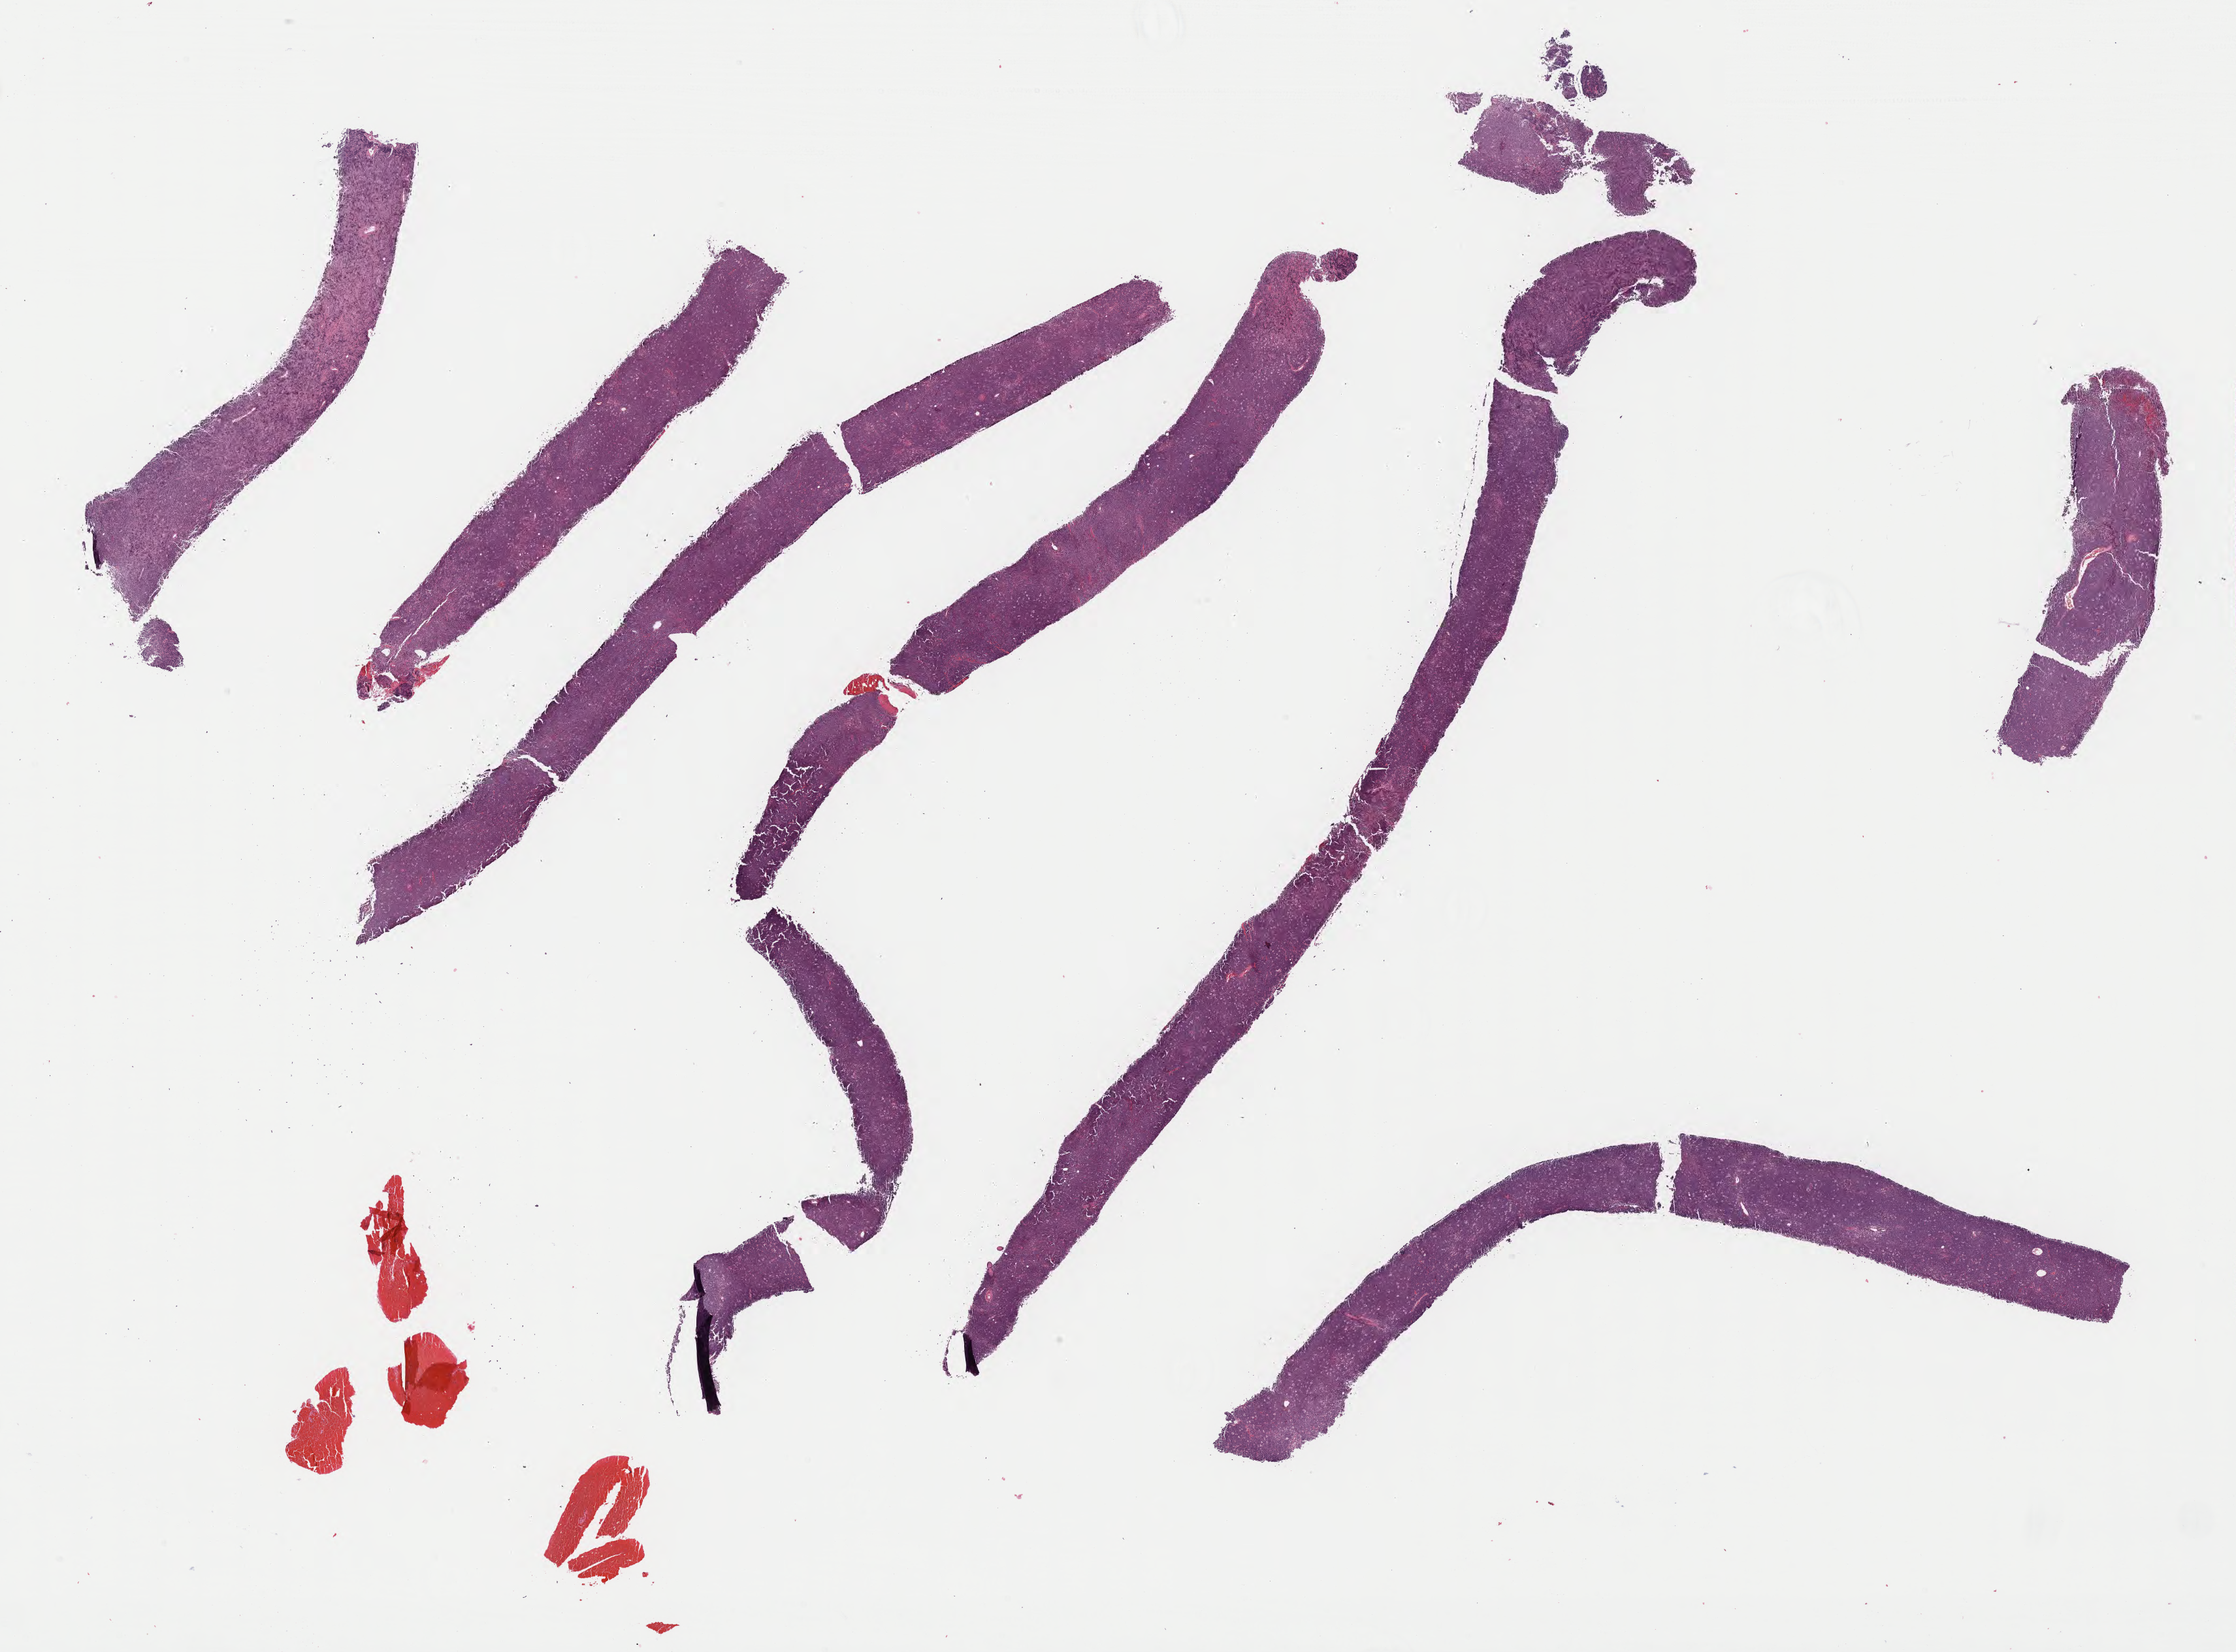
Digitized hematoxylin and eosin (H&E)-stained section, a low-resolution overview of the entire scanned area, about 27.7 x 20.5 mm, specimen: tumor tissue. Patient male; 29 years old.
• diagnosis: Burkitt lymphoma, NOS